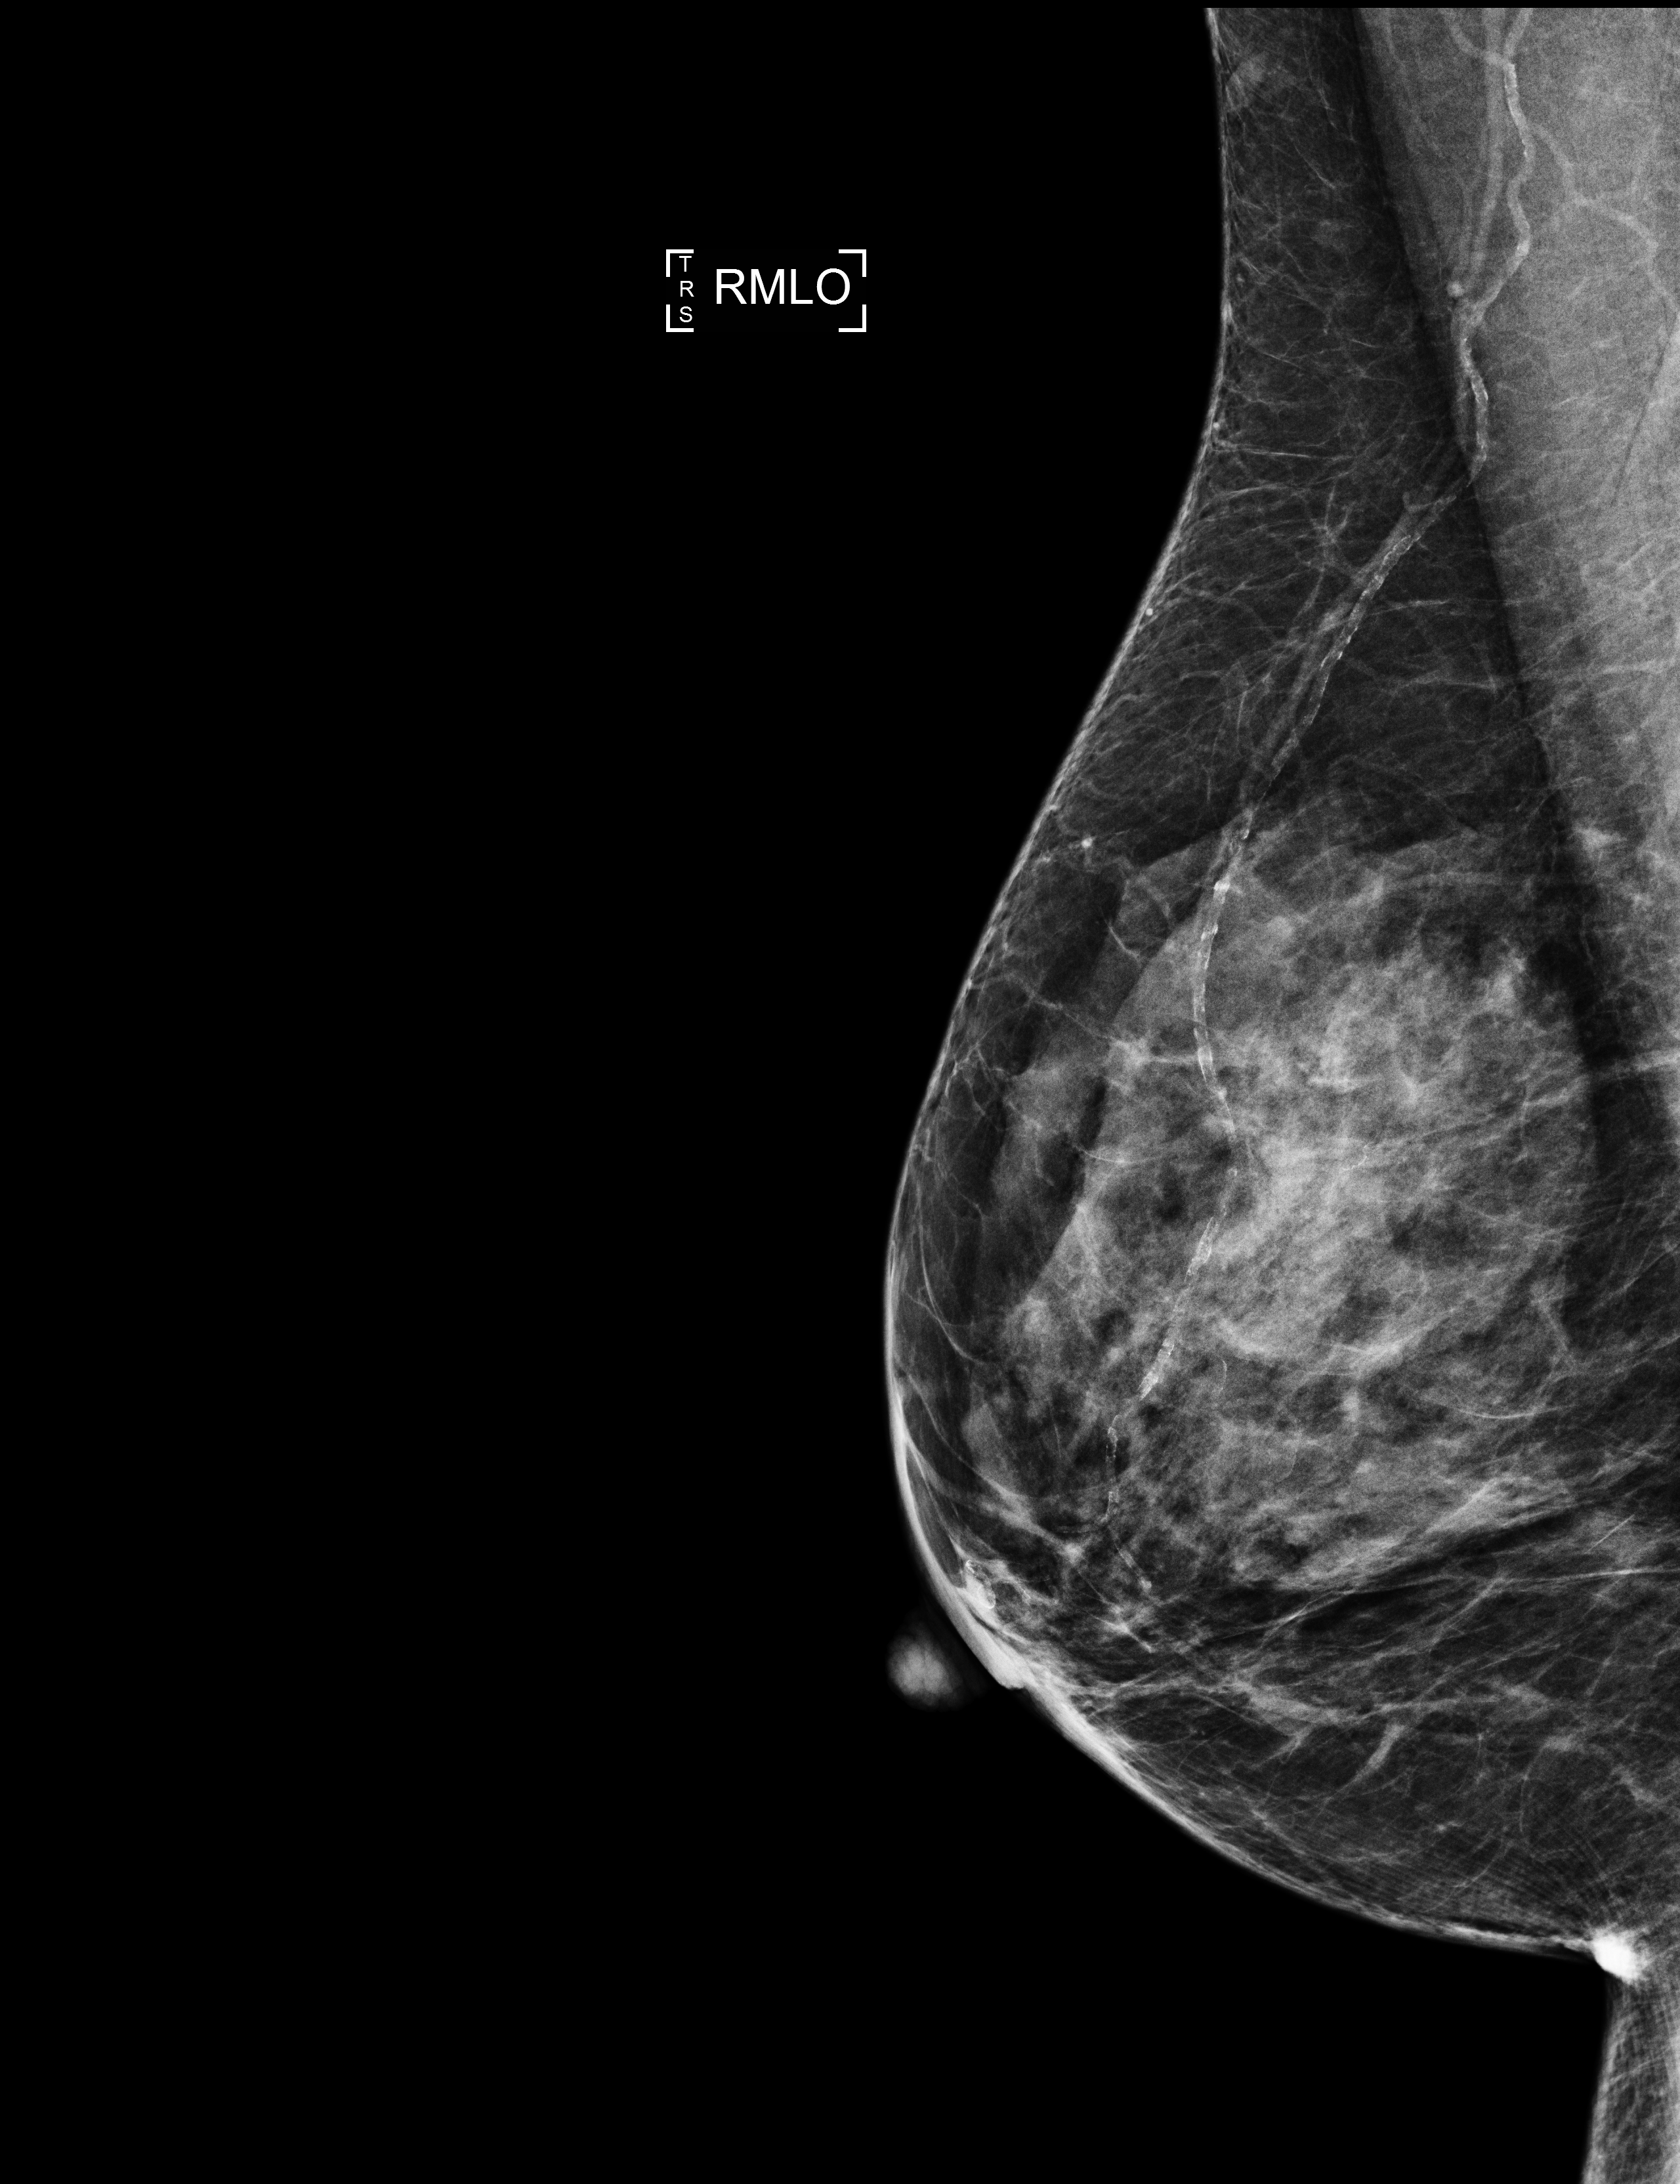
Digital mammogram (FFDM), right breast, MLO view, screening examination, compressed breast thickness 41 mm. Female patient, age 75 years.
BI-RADS breast density category at the screening exam (both breasts, scale 1–4): 3. Final BI-RADS category for the screening round (tomosynthesis exam, both breasts): category 1. Recall: no recall after this screen.